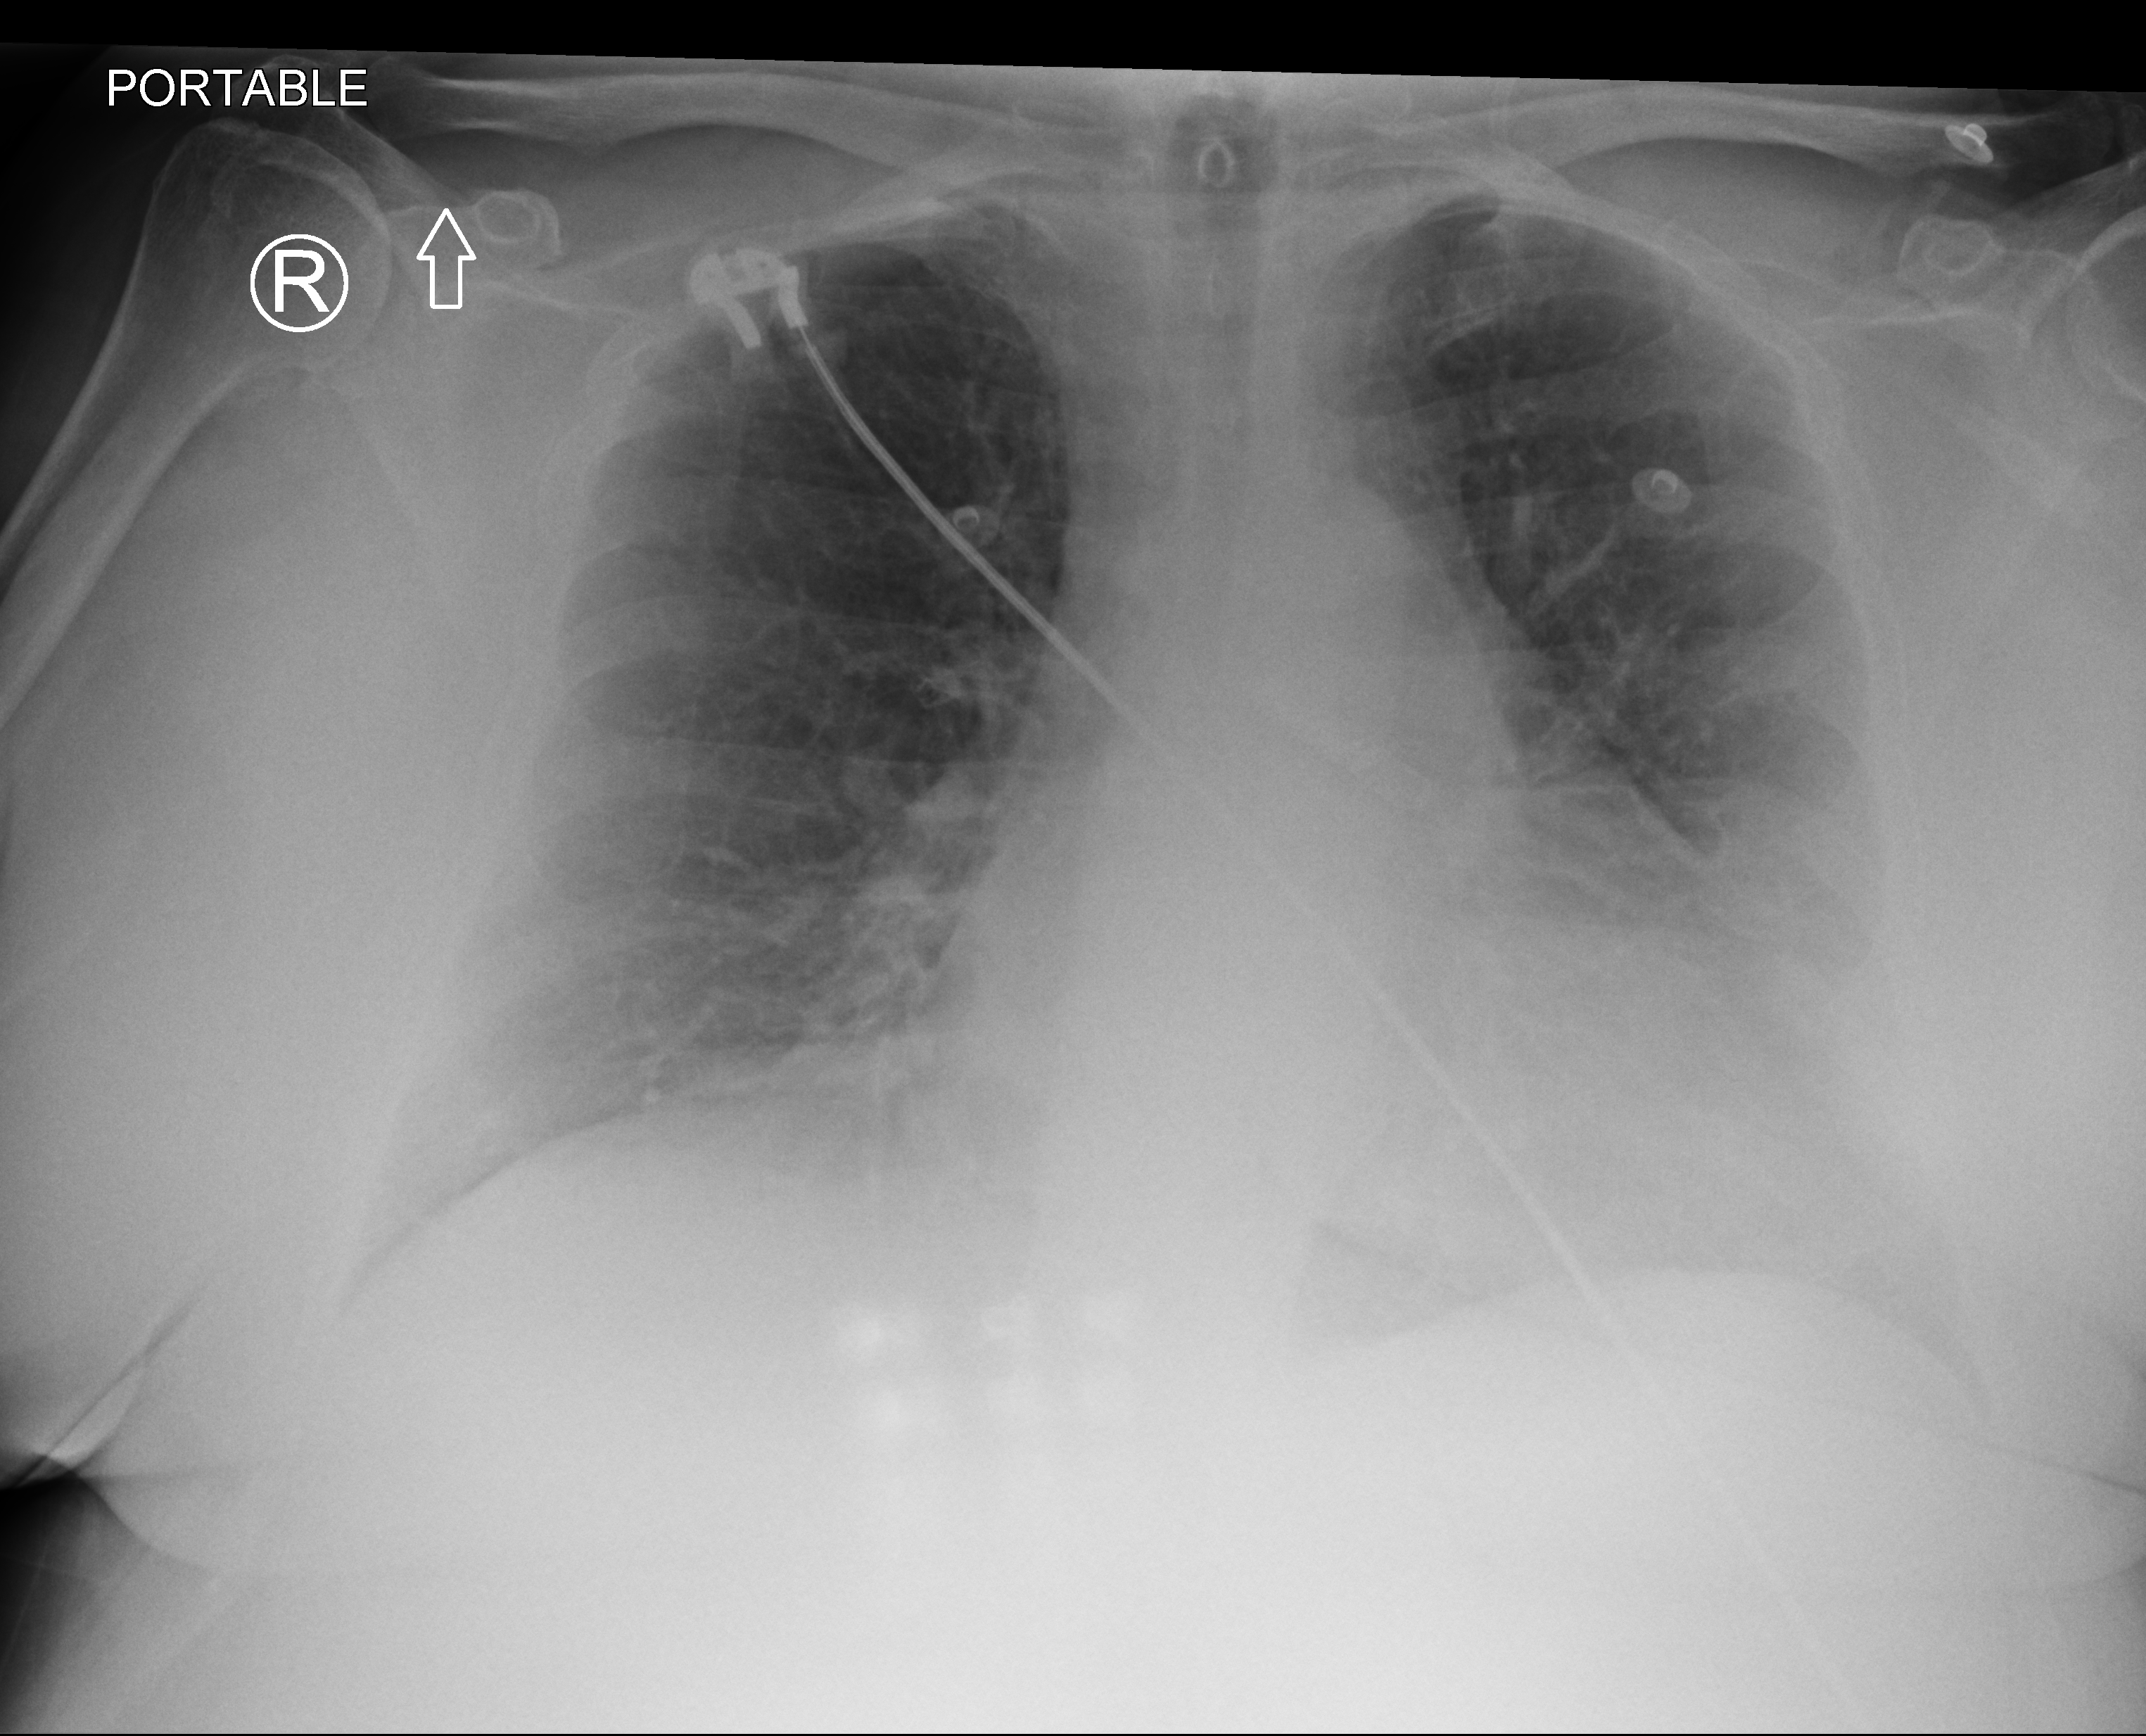
Portable chest radiograph, anteroposterior (AP) projection. Female patient hospitalised with COVID-19, age 60–74 years.
Hospital-stay facts (about this admission, not read from this image; timing relative to this image not recorded):
- chronic kidney disease (admission record): no
- other chronic lung disease (admission record): yes